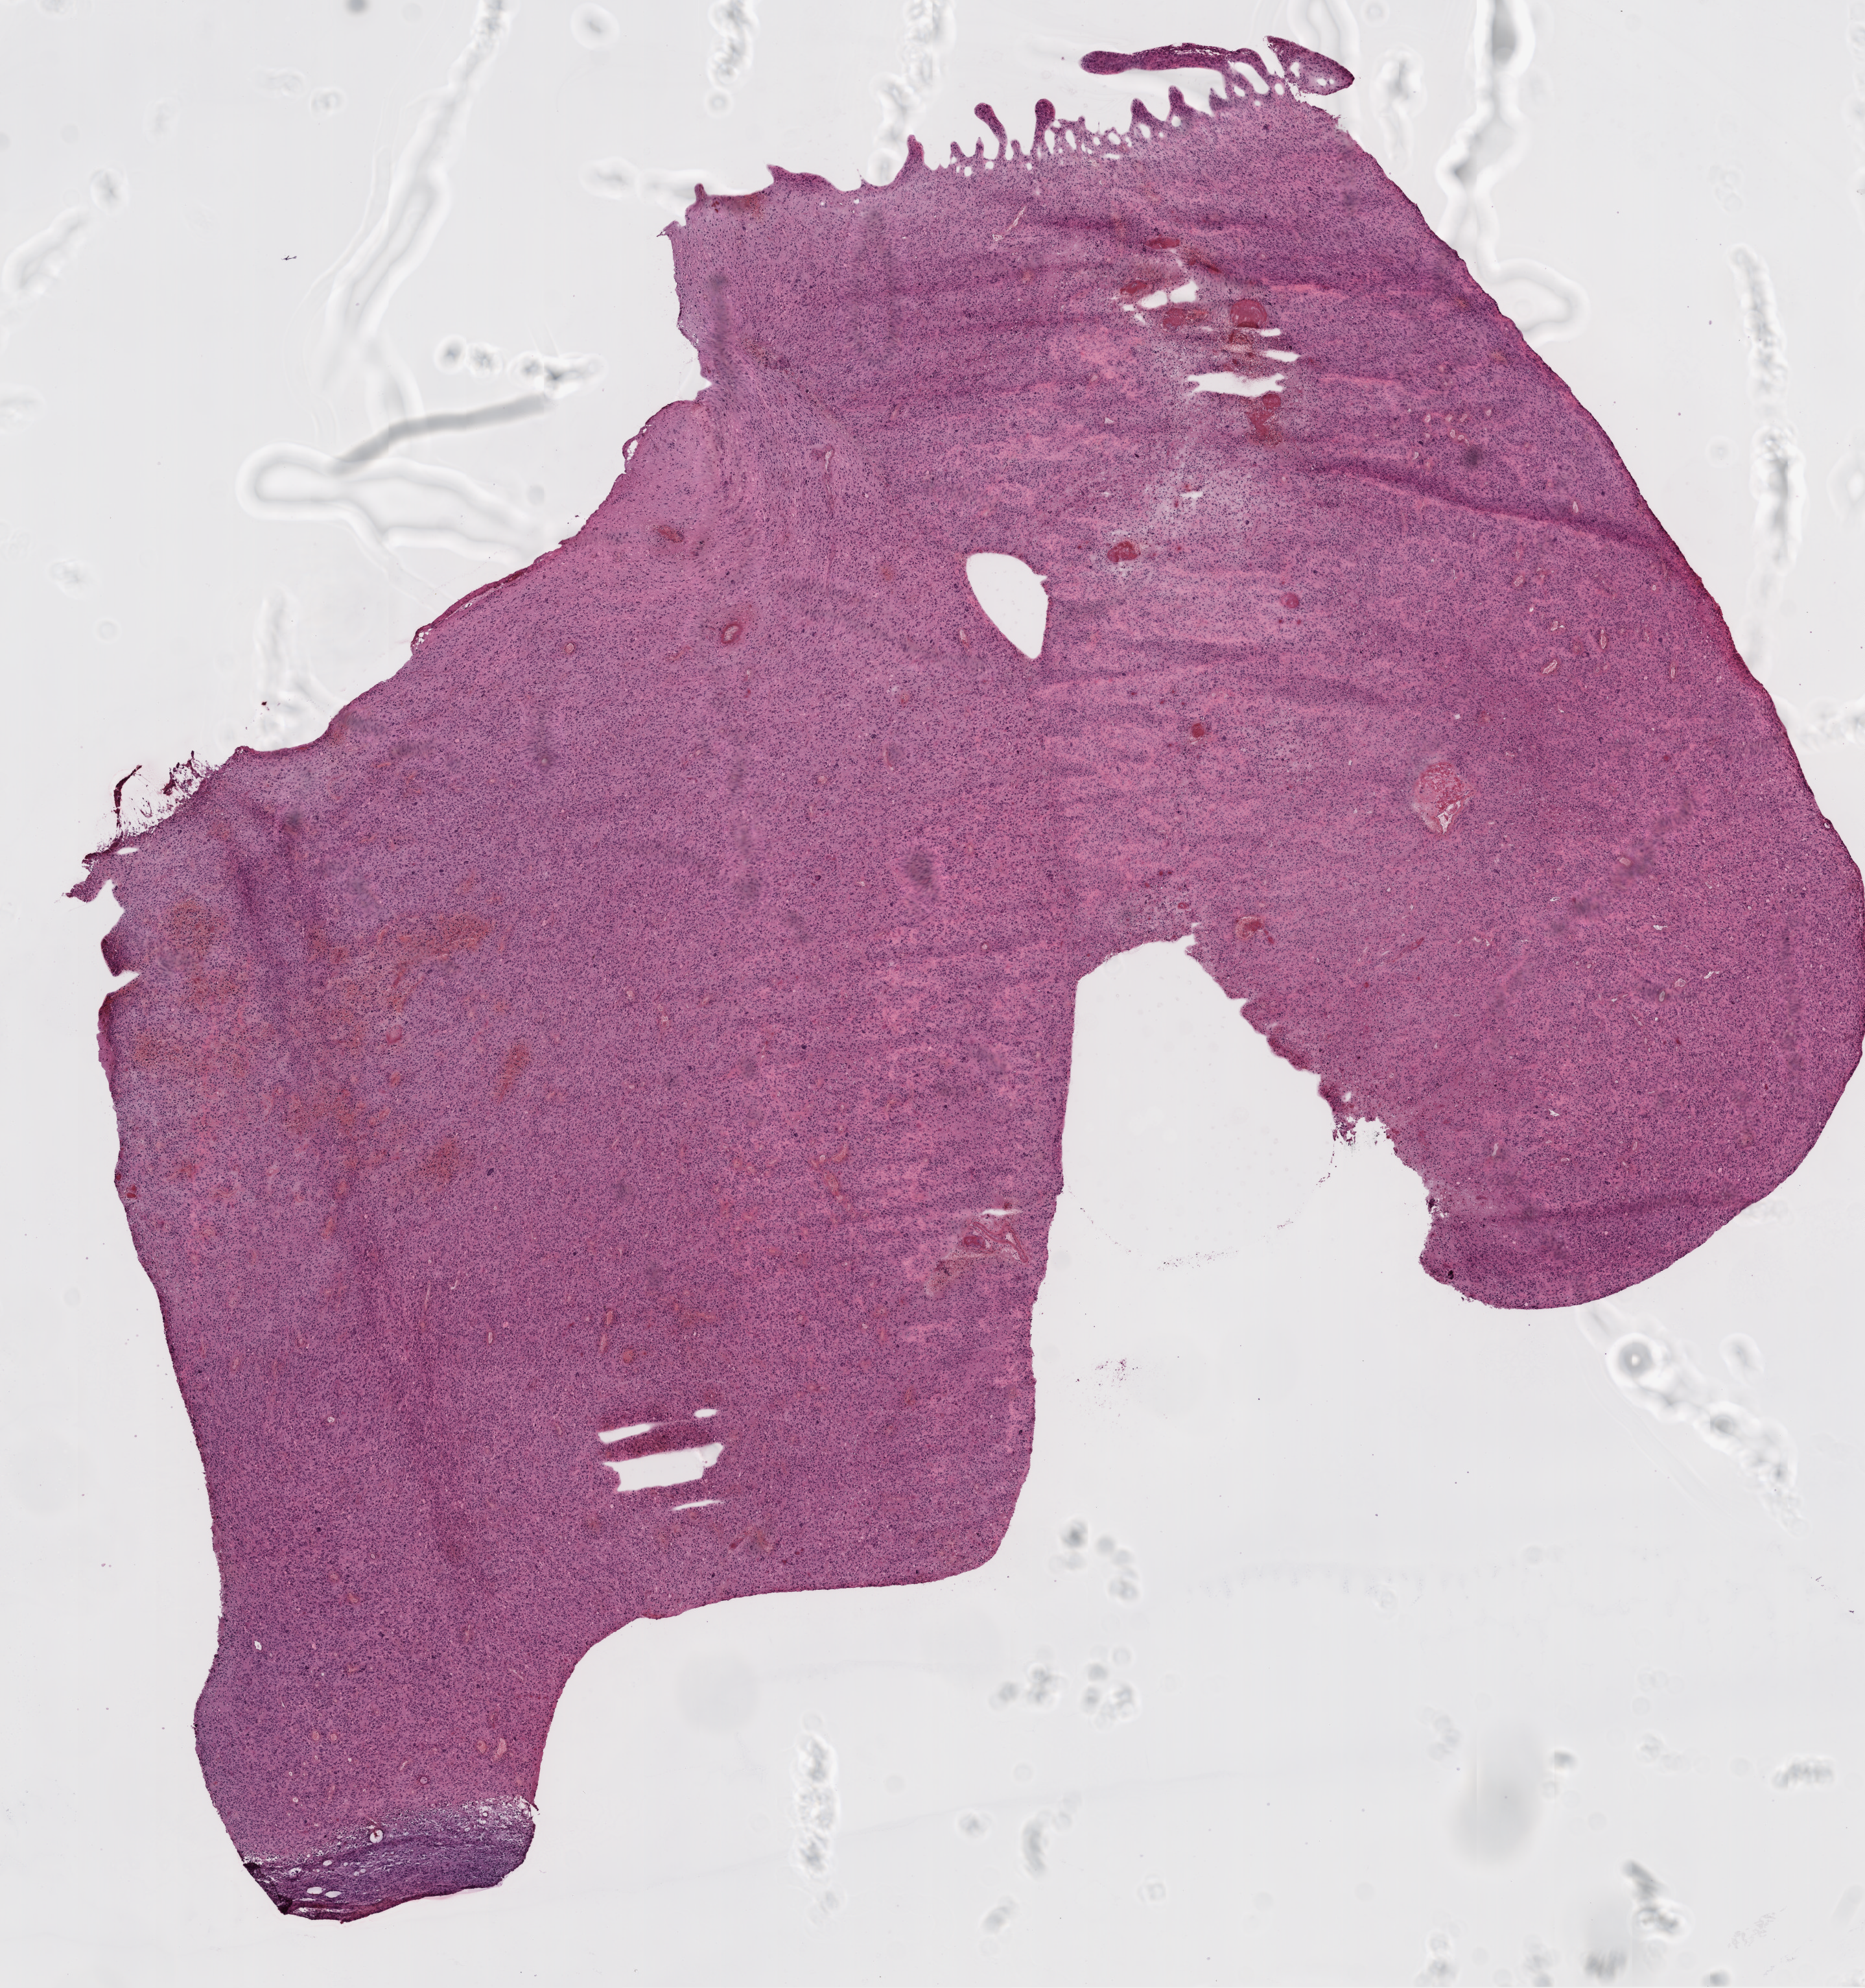
Digitized H&E tissue section (whole slide), a low-resolution overview of the entire scanned area, about 11.6 x 12.4 mm (from a 20x scan); frozen section from the top of the tissue portion; brain, primary tumour sample. Male, age 49 years at initial diagnosis. Pathologist review of this section (percent, as recorded): tumour cells 97%, tumour nuclei 100%, normal cells 0%, stromal cells 0%, necrosis 3%.
• diagnosis: Glioblastoma